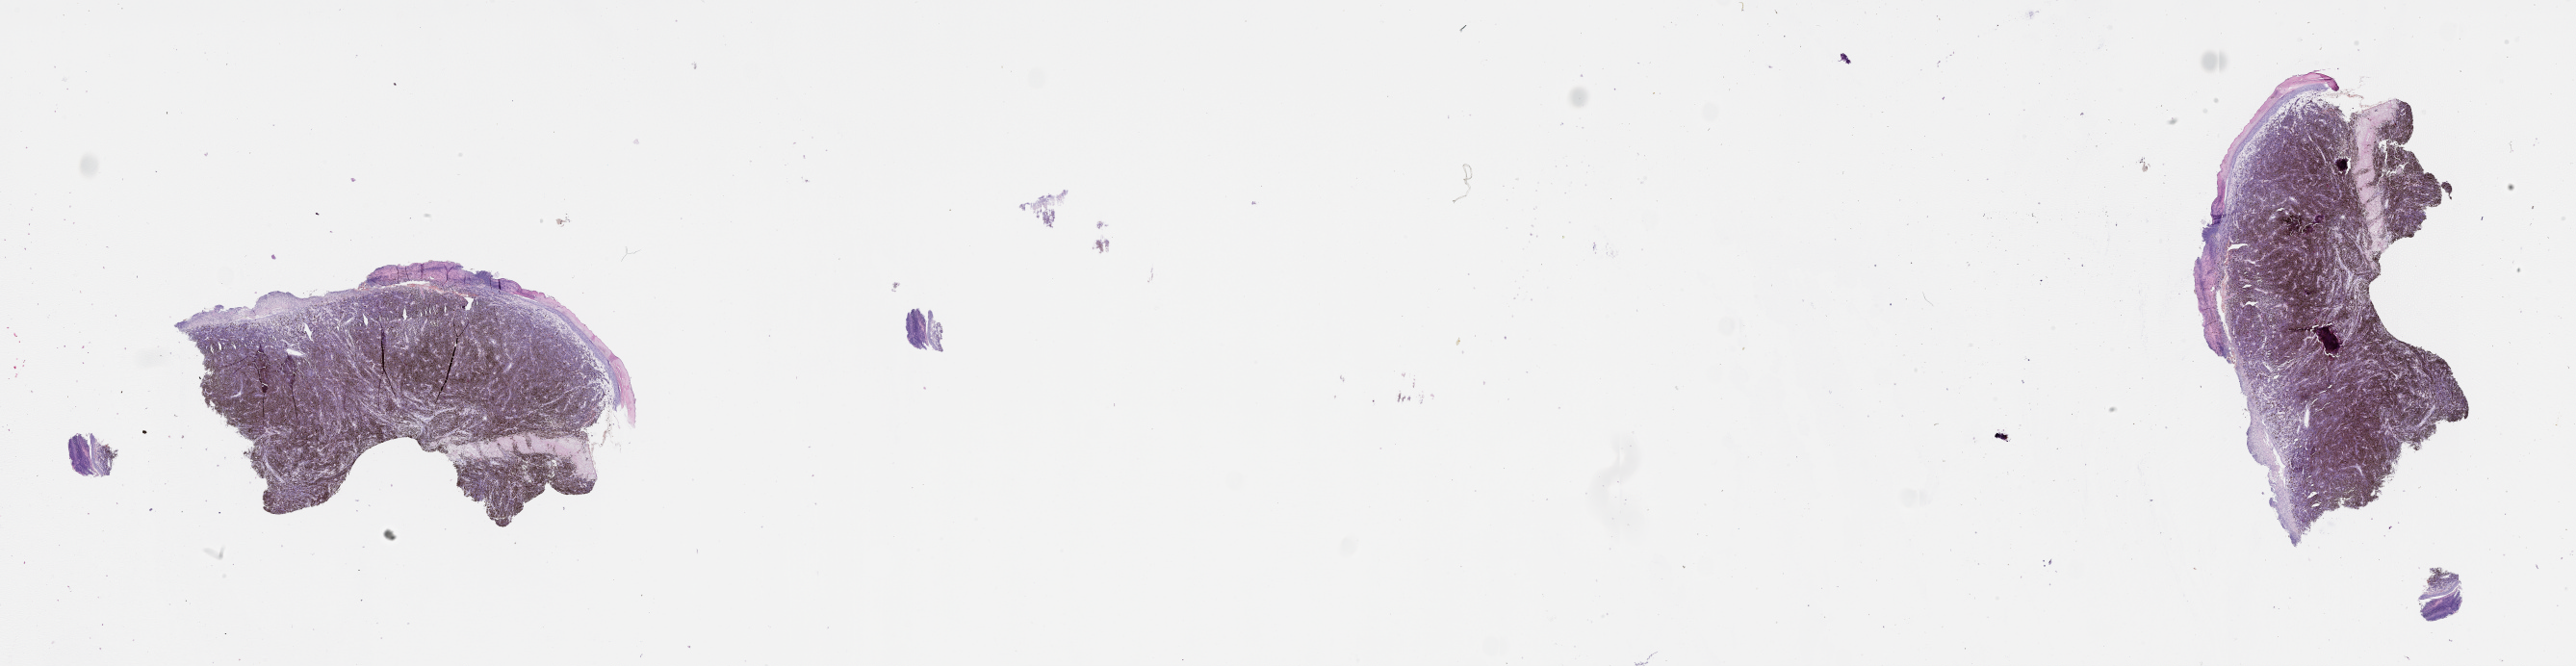
Whole-slide histology image, Hematoxylin and eosin (H&E) stained, shown as a low-resolution overview of the whole scanned area (about 43.1 x 11.1 mm, slide scanned at 20x). Tumour tissue sample, sampled site: trunk. Patient: male, age 82 years. Slide review estimates, as recorded: tumour nuclei 80%, necrosis 0%.
AJCC pathologic stage: IIC. Histologic diagnosis: Malignant melanoma, NOS.